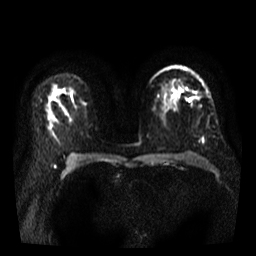
Breast MRI, one axial slice; slice 23 of 35 in the series (ordered by position); diffusion-weighted series; image 2 of 4 stored at this slice position (different b-values; order by instance number); 3 T; 5 mm slice thickness; 256 × 256 image matrix. Female patient.
Annotated regions visible in this slice (outlined manually by an expert reader):
- tumour on diffusion-weighted imaging: box from (x=171, y=89) to (x=182, y=100) px